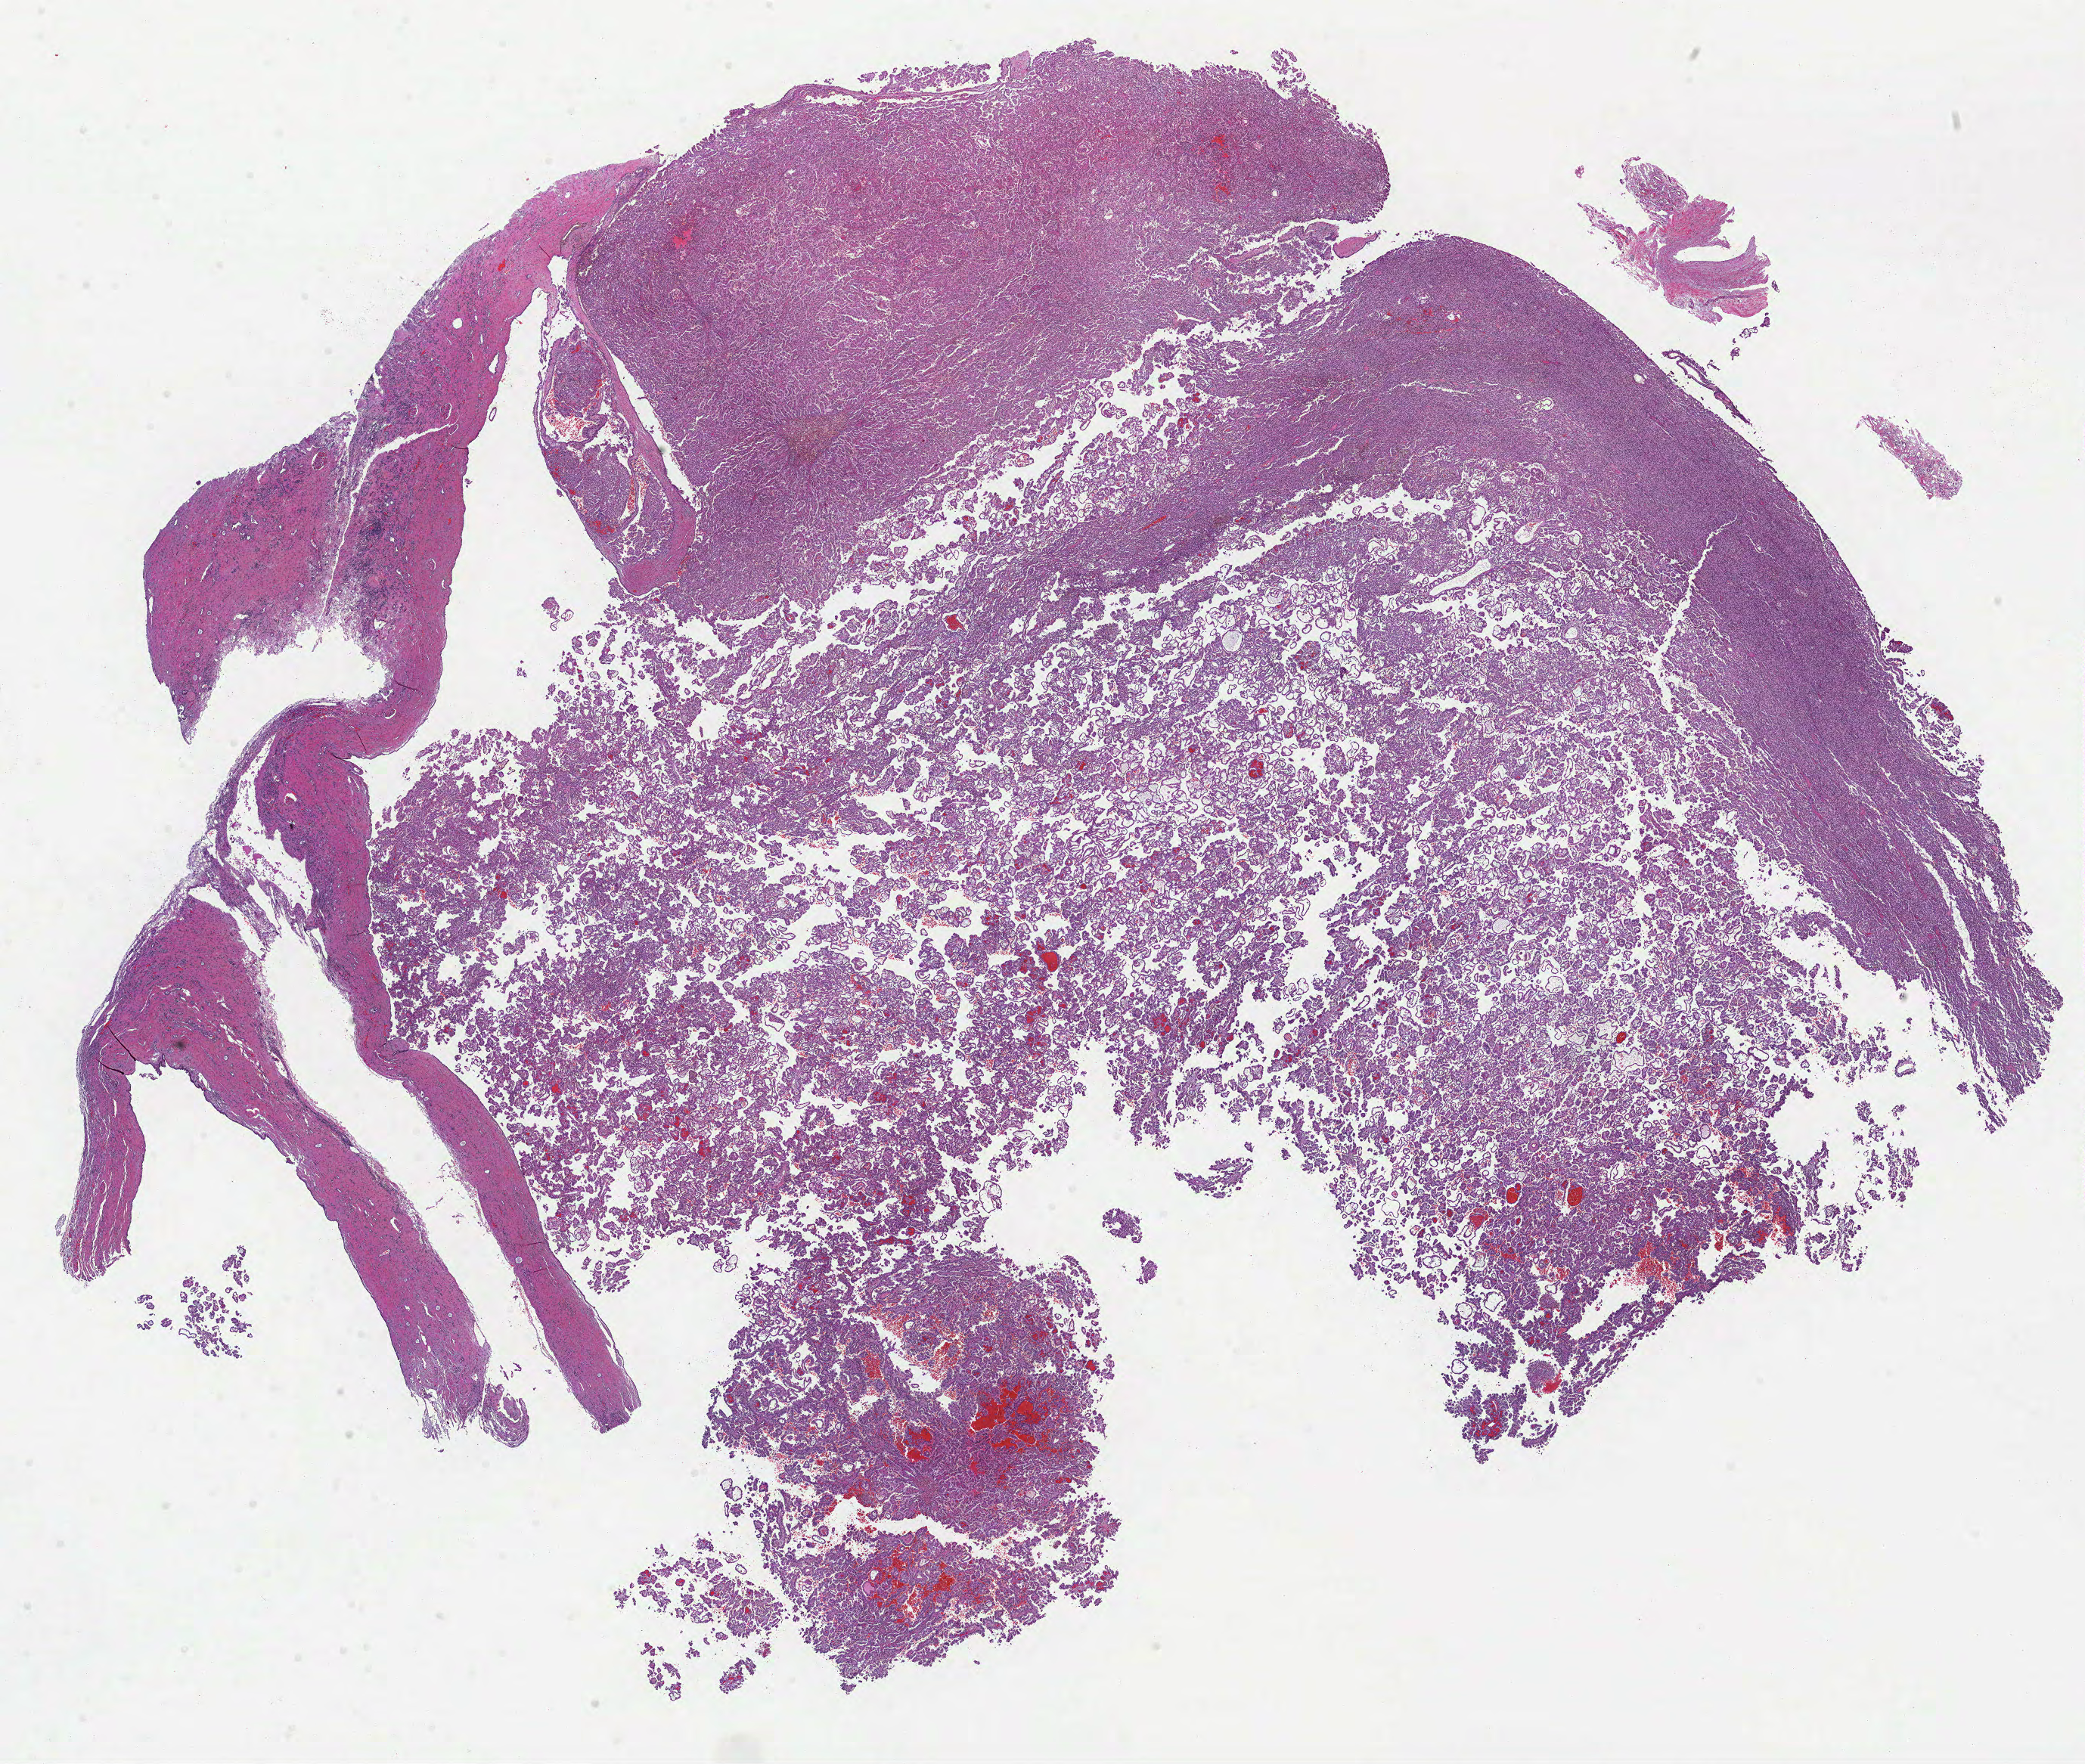
Whole-slide histology image, H&E, shown as a low-resolution overview of the whole scanned area (about 22.2 x 18.8 mm, slide scanned at 40x), formalin-fixed paraffin-embedded (FFPE) diagnostic section, sample: primary tumour, kidney. Male, age 60 years at initial diagnosis.
TNM: T1b NX MX. AJCC pathologic stage: I (7th edition). Laterality: right. Diagnosis: Papillary adenocarcinoma, NOS.